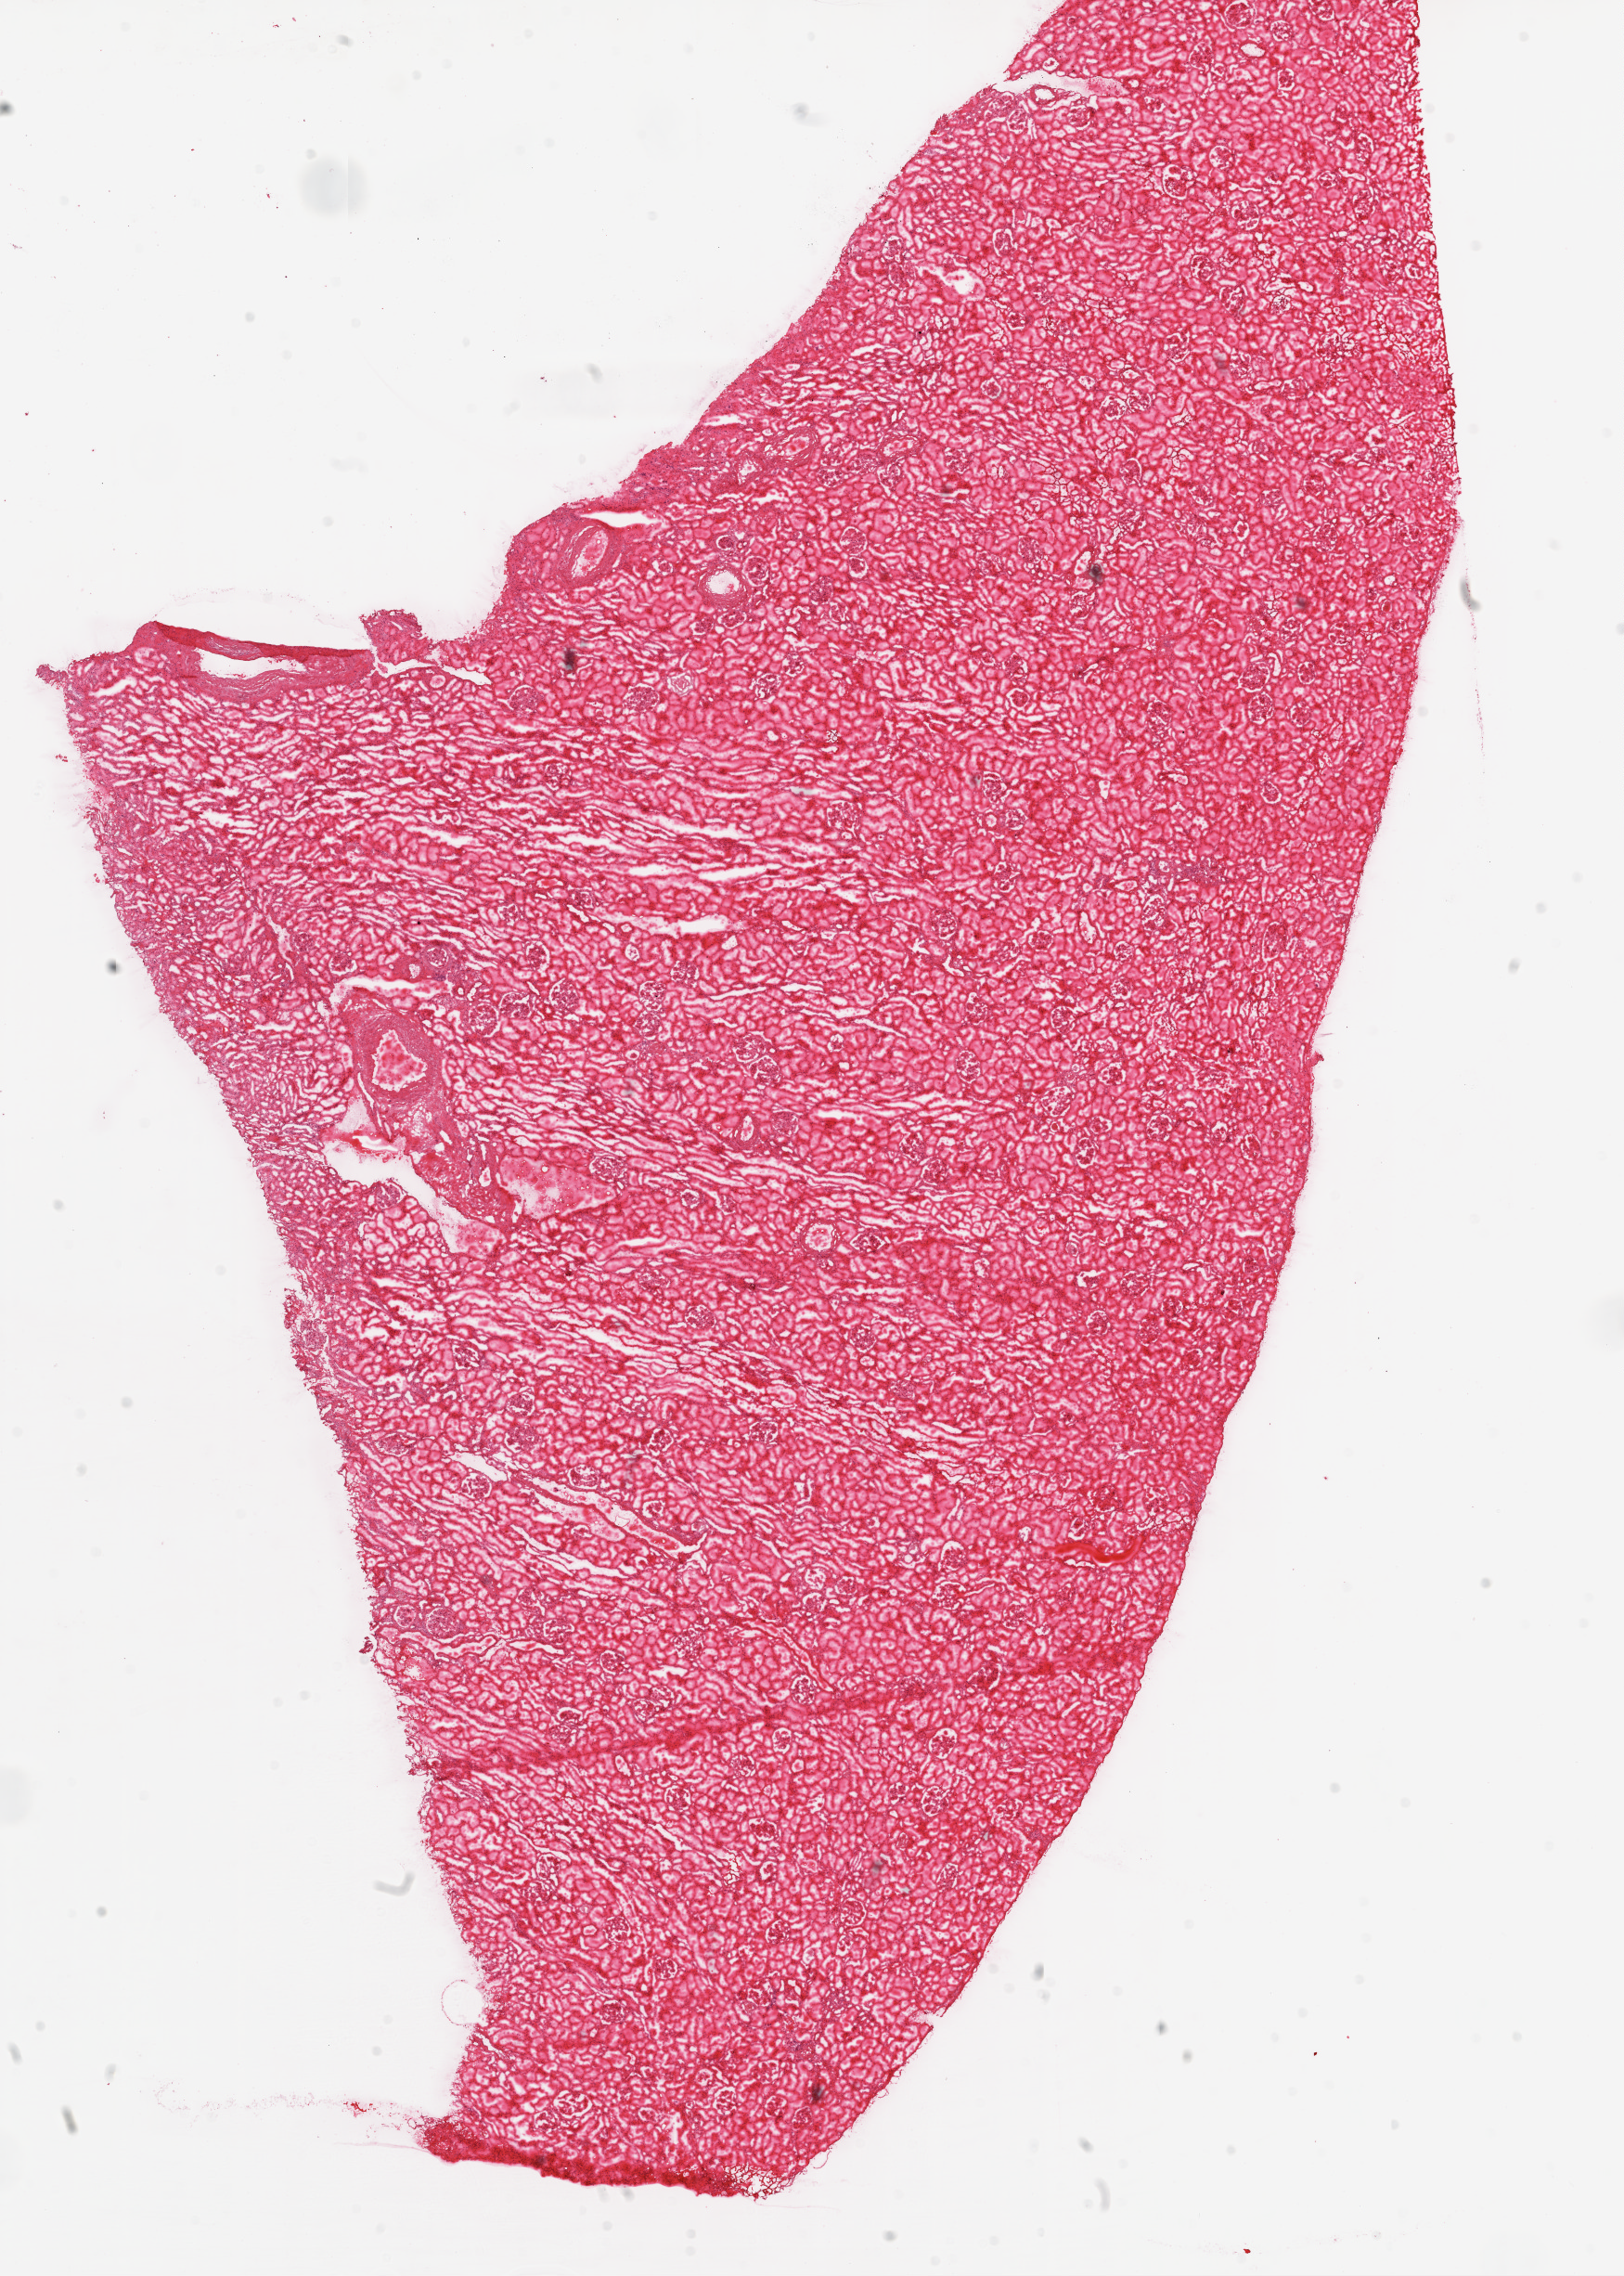
Digitized Hematoxylin and eosin (H&E) stained tissue section (whole slide), a low-resolution overview of the entire scanned area, about 14.0 x 19.7 mm (from a 20x scan). Frozen section from the top of the tissue portion. Kidney, solid tissue normal (non-tumour tissue) sample. Patient: male, age at initial diagnosis 69 years.
- this section: solid tissue normal (non-tumour) sample from the same patient
- patient diagnosis: Clear cell adenocarcinoma, NOS